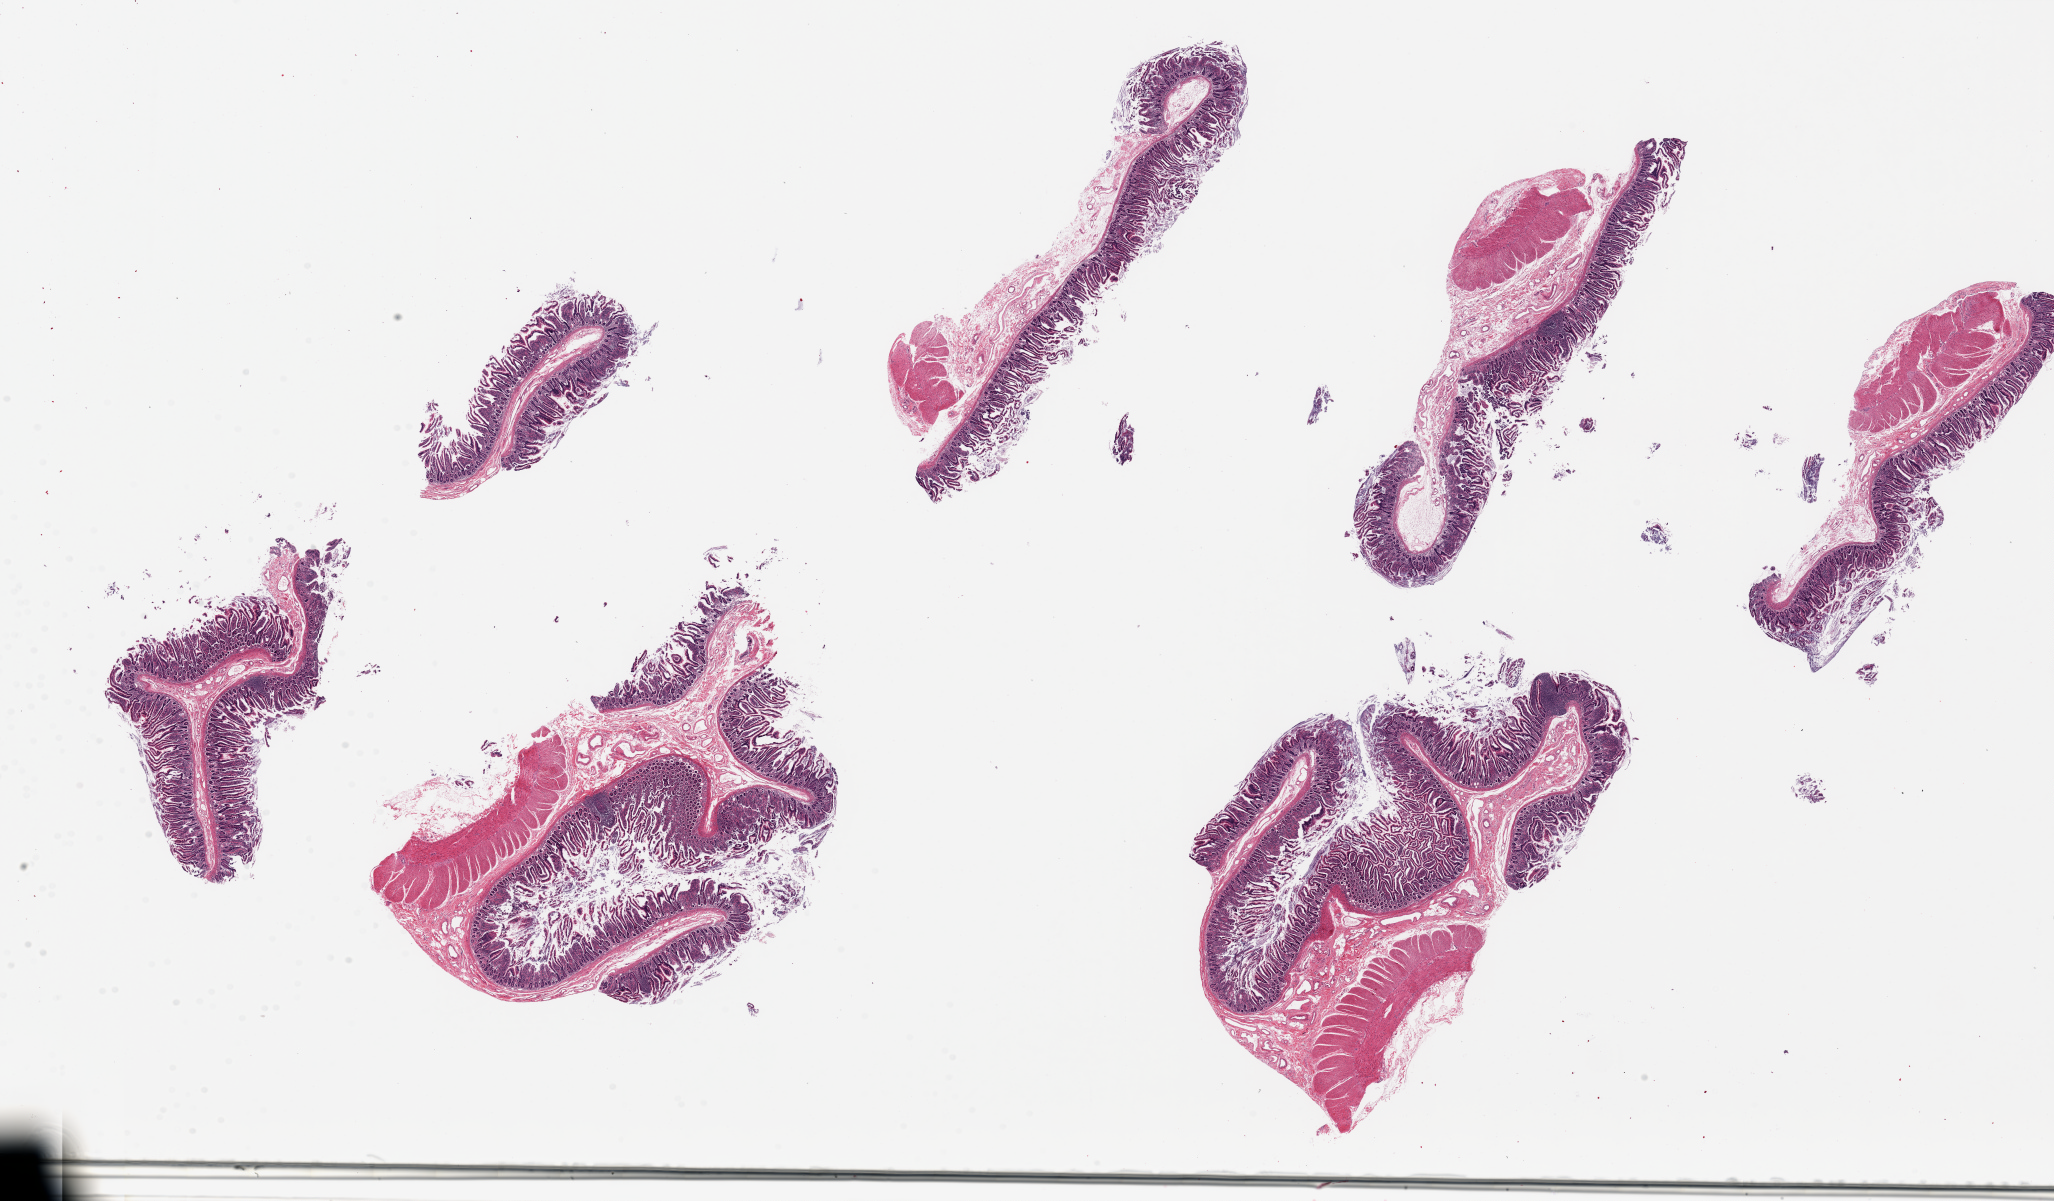
Whole-slide image, haematoxylin and eosin stain, brightfield — low-resolution overview of the scanned area, about 32.5 x 19.0 mm. PAXgene-fixed paraffin-embedded (PFPE) section. Section of ileum (target tissue). Tissue donor sample. Donor sex: male.
Review note (as recorded): 6 pieces ~7x2mm, ~50% mucosa/stroma.